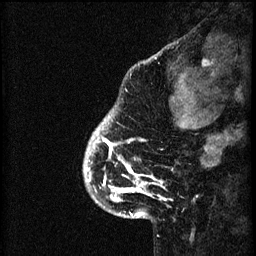
Breast MRI (dynamic contrast-enhanced), one sagittal slice. Slice 9 of 60 in the series (ordered by position). 3 images stored at this slice position (order not interpretable as contrast timing). 1.5 T. TE 4.2 ms, TR 8.2 ms. 2 mm slice thickness. 256 × 256 image matrix. Female patient, age 41 years.
Annotated regions visible in this slice (semi-automatic segmentation, software-assisted and operator-edited):
- analysis volume of interest (the breast-tissue region the enhancement analysis was run in; not a lesion): box from (x=85, y=108) to (x=176, y=205) px
- tumour enhancement mask (voxels above the 70 % enhancement threshold inside the analysis volume of interest): (x=85, y=116)–(x=166, y=203)